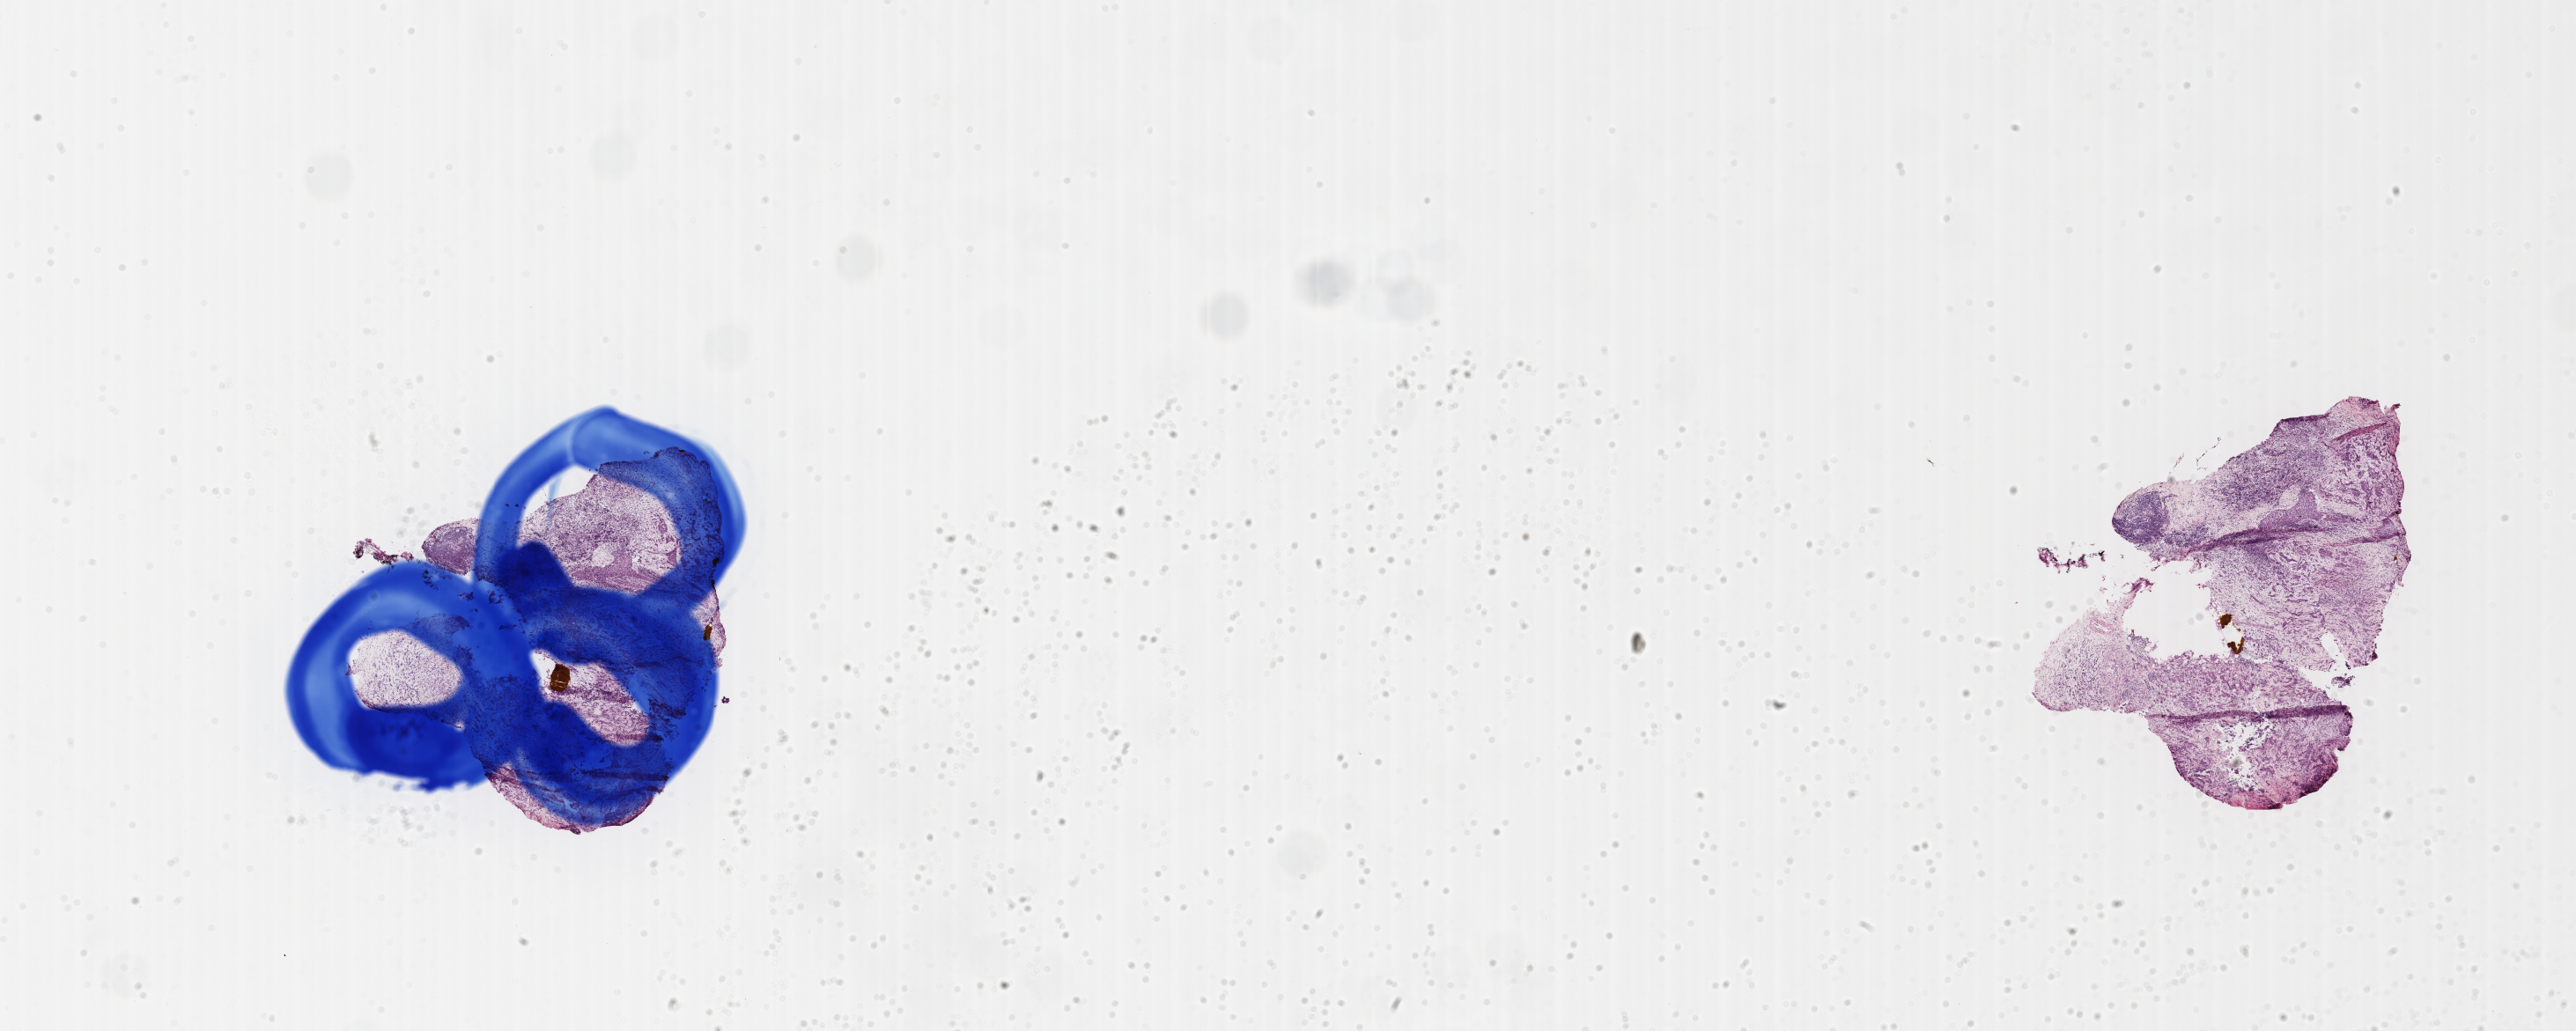
Whole-slide image, hematoxylin and eosin (H&E) stain, whole scanned area (about 23.6 x 9.4 mm) shown as a low-resolution overview, cryosection, specimen: primary tumor, site: breast (right). Female patient; age at initial diagnosis 69 years. Composition of this section per pathologist review: tumor cells 75%, tumor nuclei 75%, stromal cells 25%, necrosis 0%, normal cells 0%. Infiltration values recorded for this section: lymphocyte infiltration 5%, monocyte infiltration 2%, neutrophil infiltration 5%.
* section: bottom of the tissue portion
* diagnosis: Infiltrating duct carcinoma, NOS